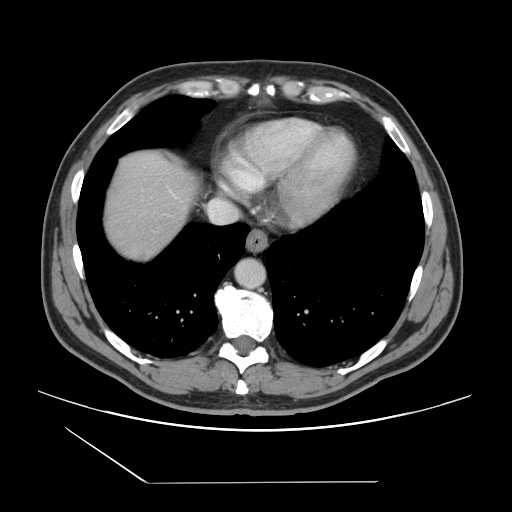
Contrast-enhanced abdominal CT, one axial slice. Position 134 of 157 along the scan axis. Intravenous contrast given. Soft-tissue window (W 400 / L 40 HU). 2.5 mm slice thickness. 512 × 512 image matrix, field of view 407 × 407 mm. Male patient, age 61 years. Case-level facts recorded for this patient, not image findings: diagnosis: colorectal cancer liver metastases, imaged before liver resection; multiple liver metastases: yes; largest metastasis: 5.5 cm.
Annotated regions visible in this slice (manually delineated by an expert):
- liver: bounding box (x1, y1, x2, y2) in pixels: (105, 155, 197, 261)
- planned liver remnant (the part of the liver to remain after resection): (105, 155, 197, 232)
- liver metastasis: (138, 252, 155, 262)